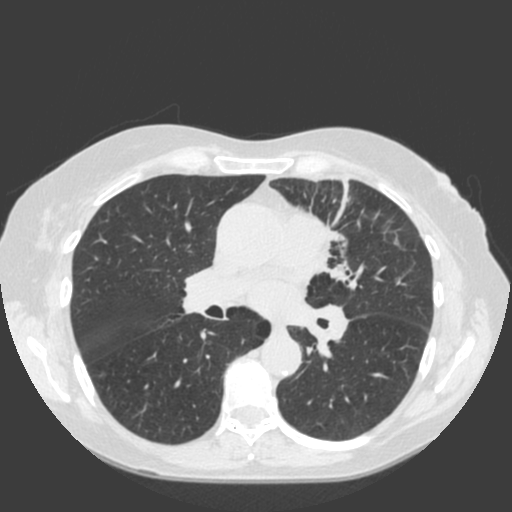
Low-dose screening chest CT, one axial slice; slice 106 of 184 in the series (ordered by position); 120 kVp; lung window (W 1500 / L -600 HU); 2 mm slice thickness; 512 × 512 image matrix, field of view 350 × 350 mm.
Outlined on this slice (manually delineated by an expert):
- lesion 1 (tumor, hilum of left lung): bounding box <328,231,365,289> (left, top, right, bottom; pixels)